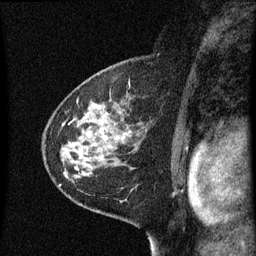
Breast MRI (dynamic contrast-enhanced), one sagittal slice; position 39 of 60 along the scan axis; dynamic contrast-enhanced series, image 2 of 3 at this slice position (ordered by acquisition); 1.5 T; TE 4.2 ms, TR 8 ms; 2 mm slice thickness; 256 × 256 image matrix, field of view 180 × 180 mm. Patient: female, 60 years.
Outlined on this slice (semi-automatic segmentation, software-assisted and operator-edited):
- analysis volume of interest (the breast-tissue region the enhancement analysis was run in; not a lesion): bounding box (x1, y1, x2, y2) in pixels: (48, 82, 149, 183)
- tumour enhancement mask (voxels above the 70 % enhancement threshold inside the analysis volume of interest): (101, 128, 104, 133)